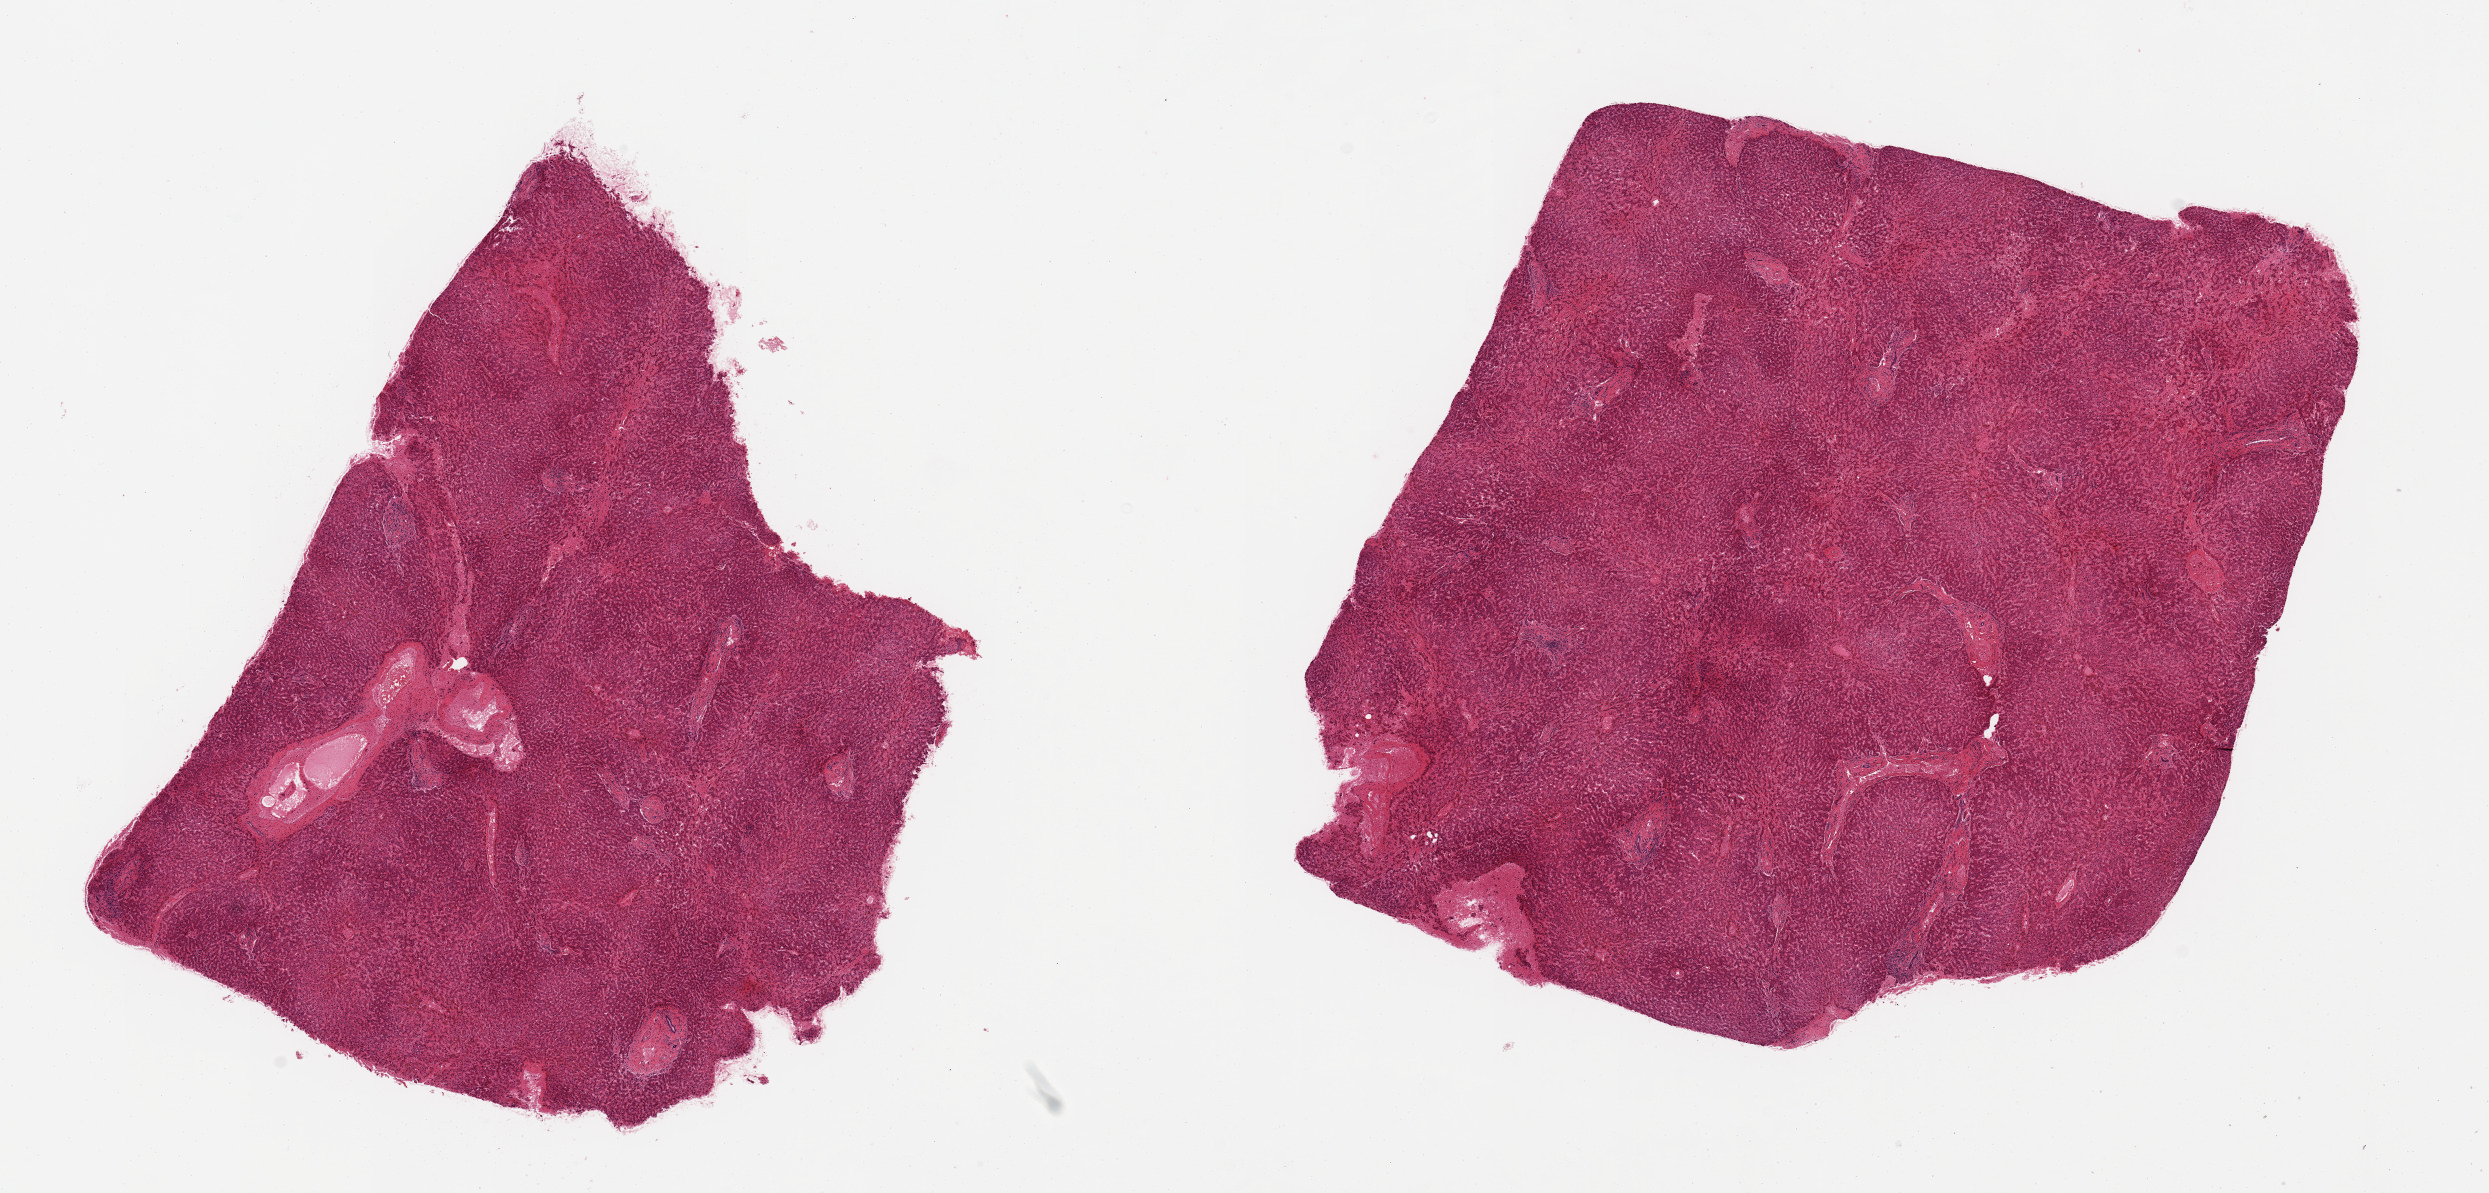
Haematoxylin and eosin whole-slide image, brightfield, whole scanned area (about 19.7 x 9.4 mm, acquisition: 20x scan) shown as a low-resolution overview, PAXgene-fixed paraffin-embedded (PFPE) section, section of liver (target tissue), tissue donor sample. Donor sex: female.
Review note (as recorded): 2 pieces; moderate congestion; severe central atrophy.